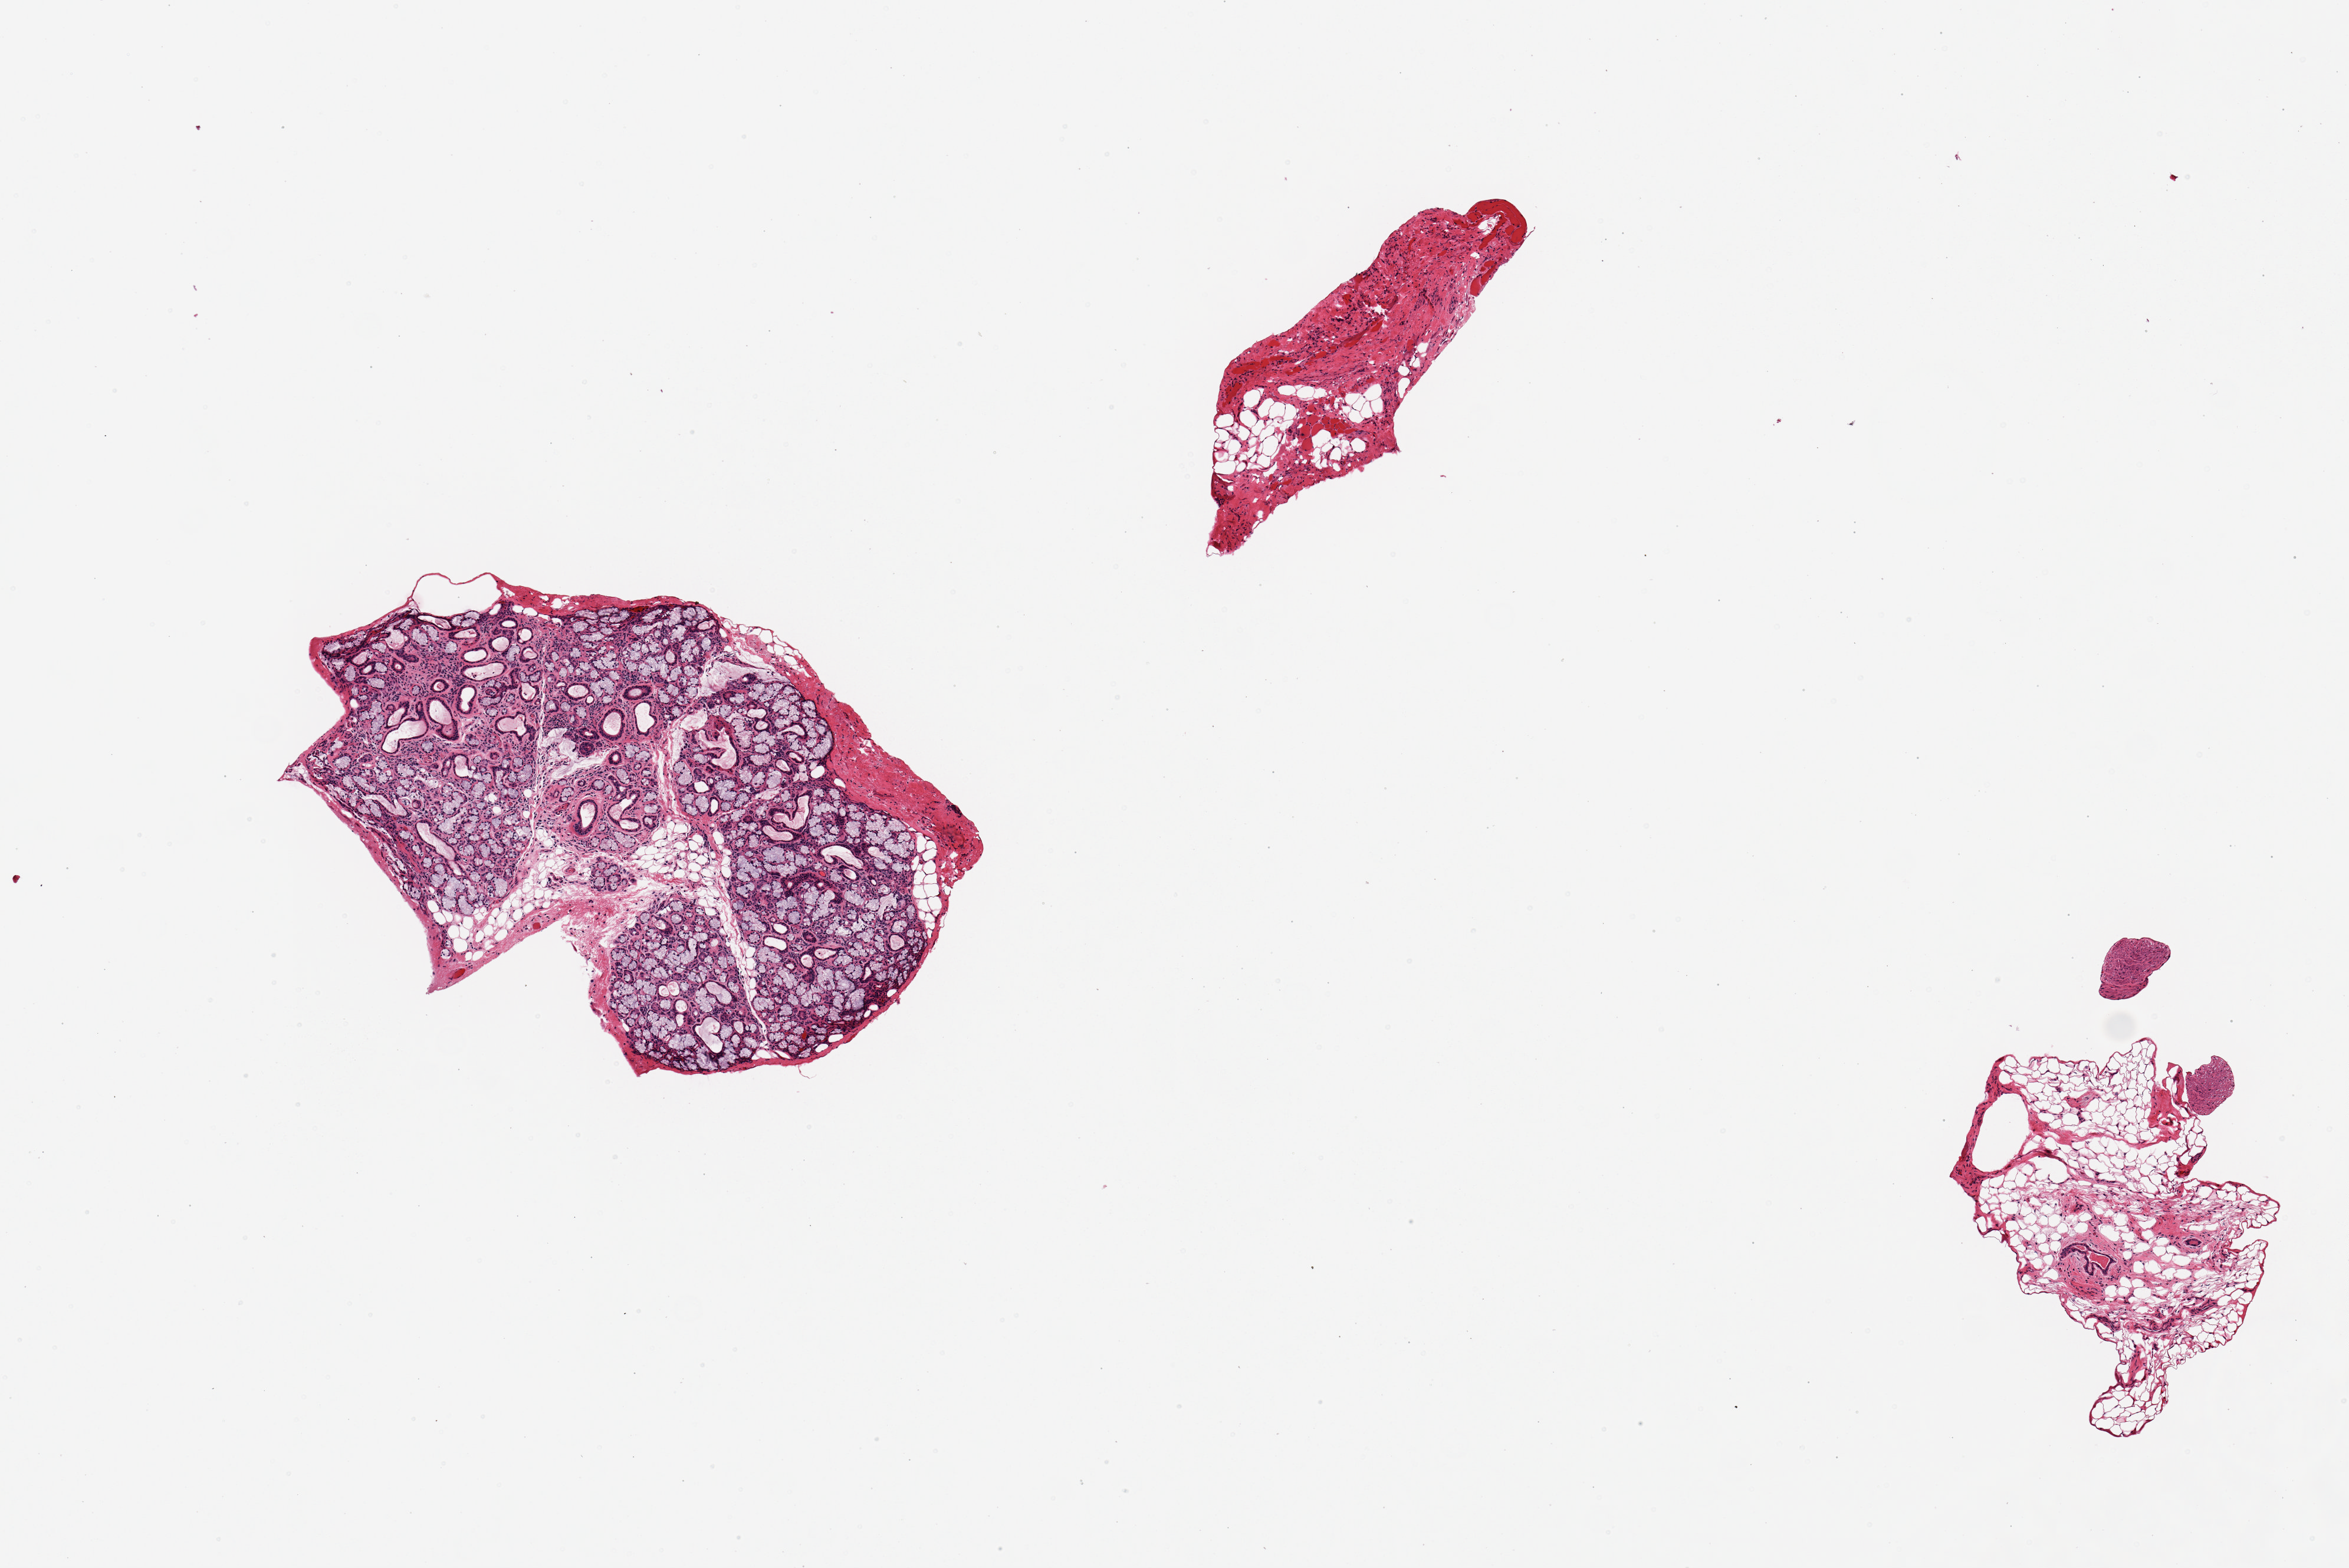
Whole-slide image, hematoxylin and eosin (H&E) stain — low-resolution overview of the scanned area, about 7.9 x 5.3 mm (slide scanned at 20x). PAXgene-fixed, paraffin-embedded tissue. Sampled site (target tissue): minor salivary gland. Tissue donor sample.
- reviewer comment on this tissue sample: 3 pieces; large piece is good gland; 2 smaller pieces are fat & stroma only